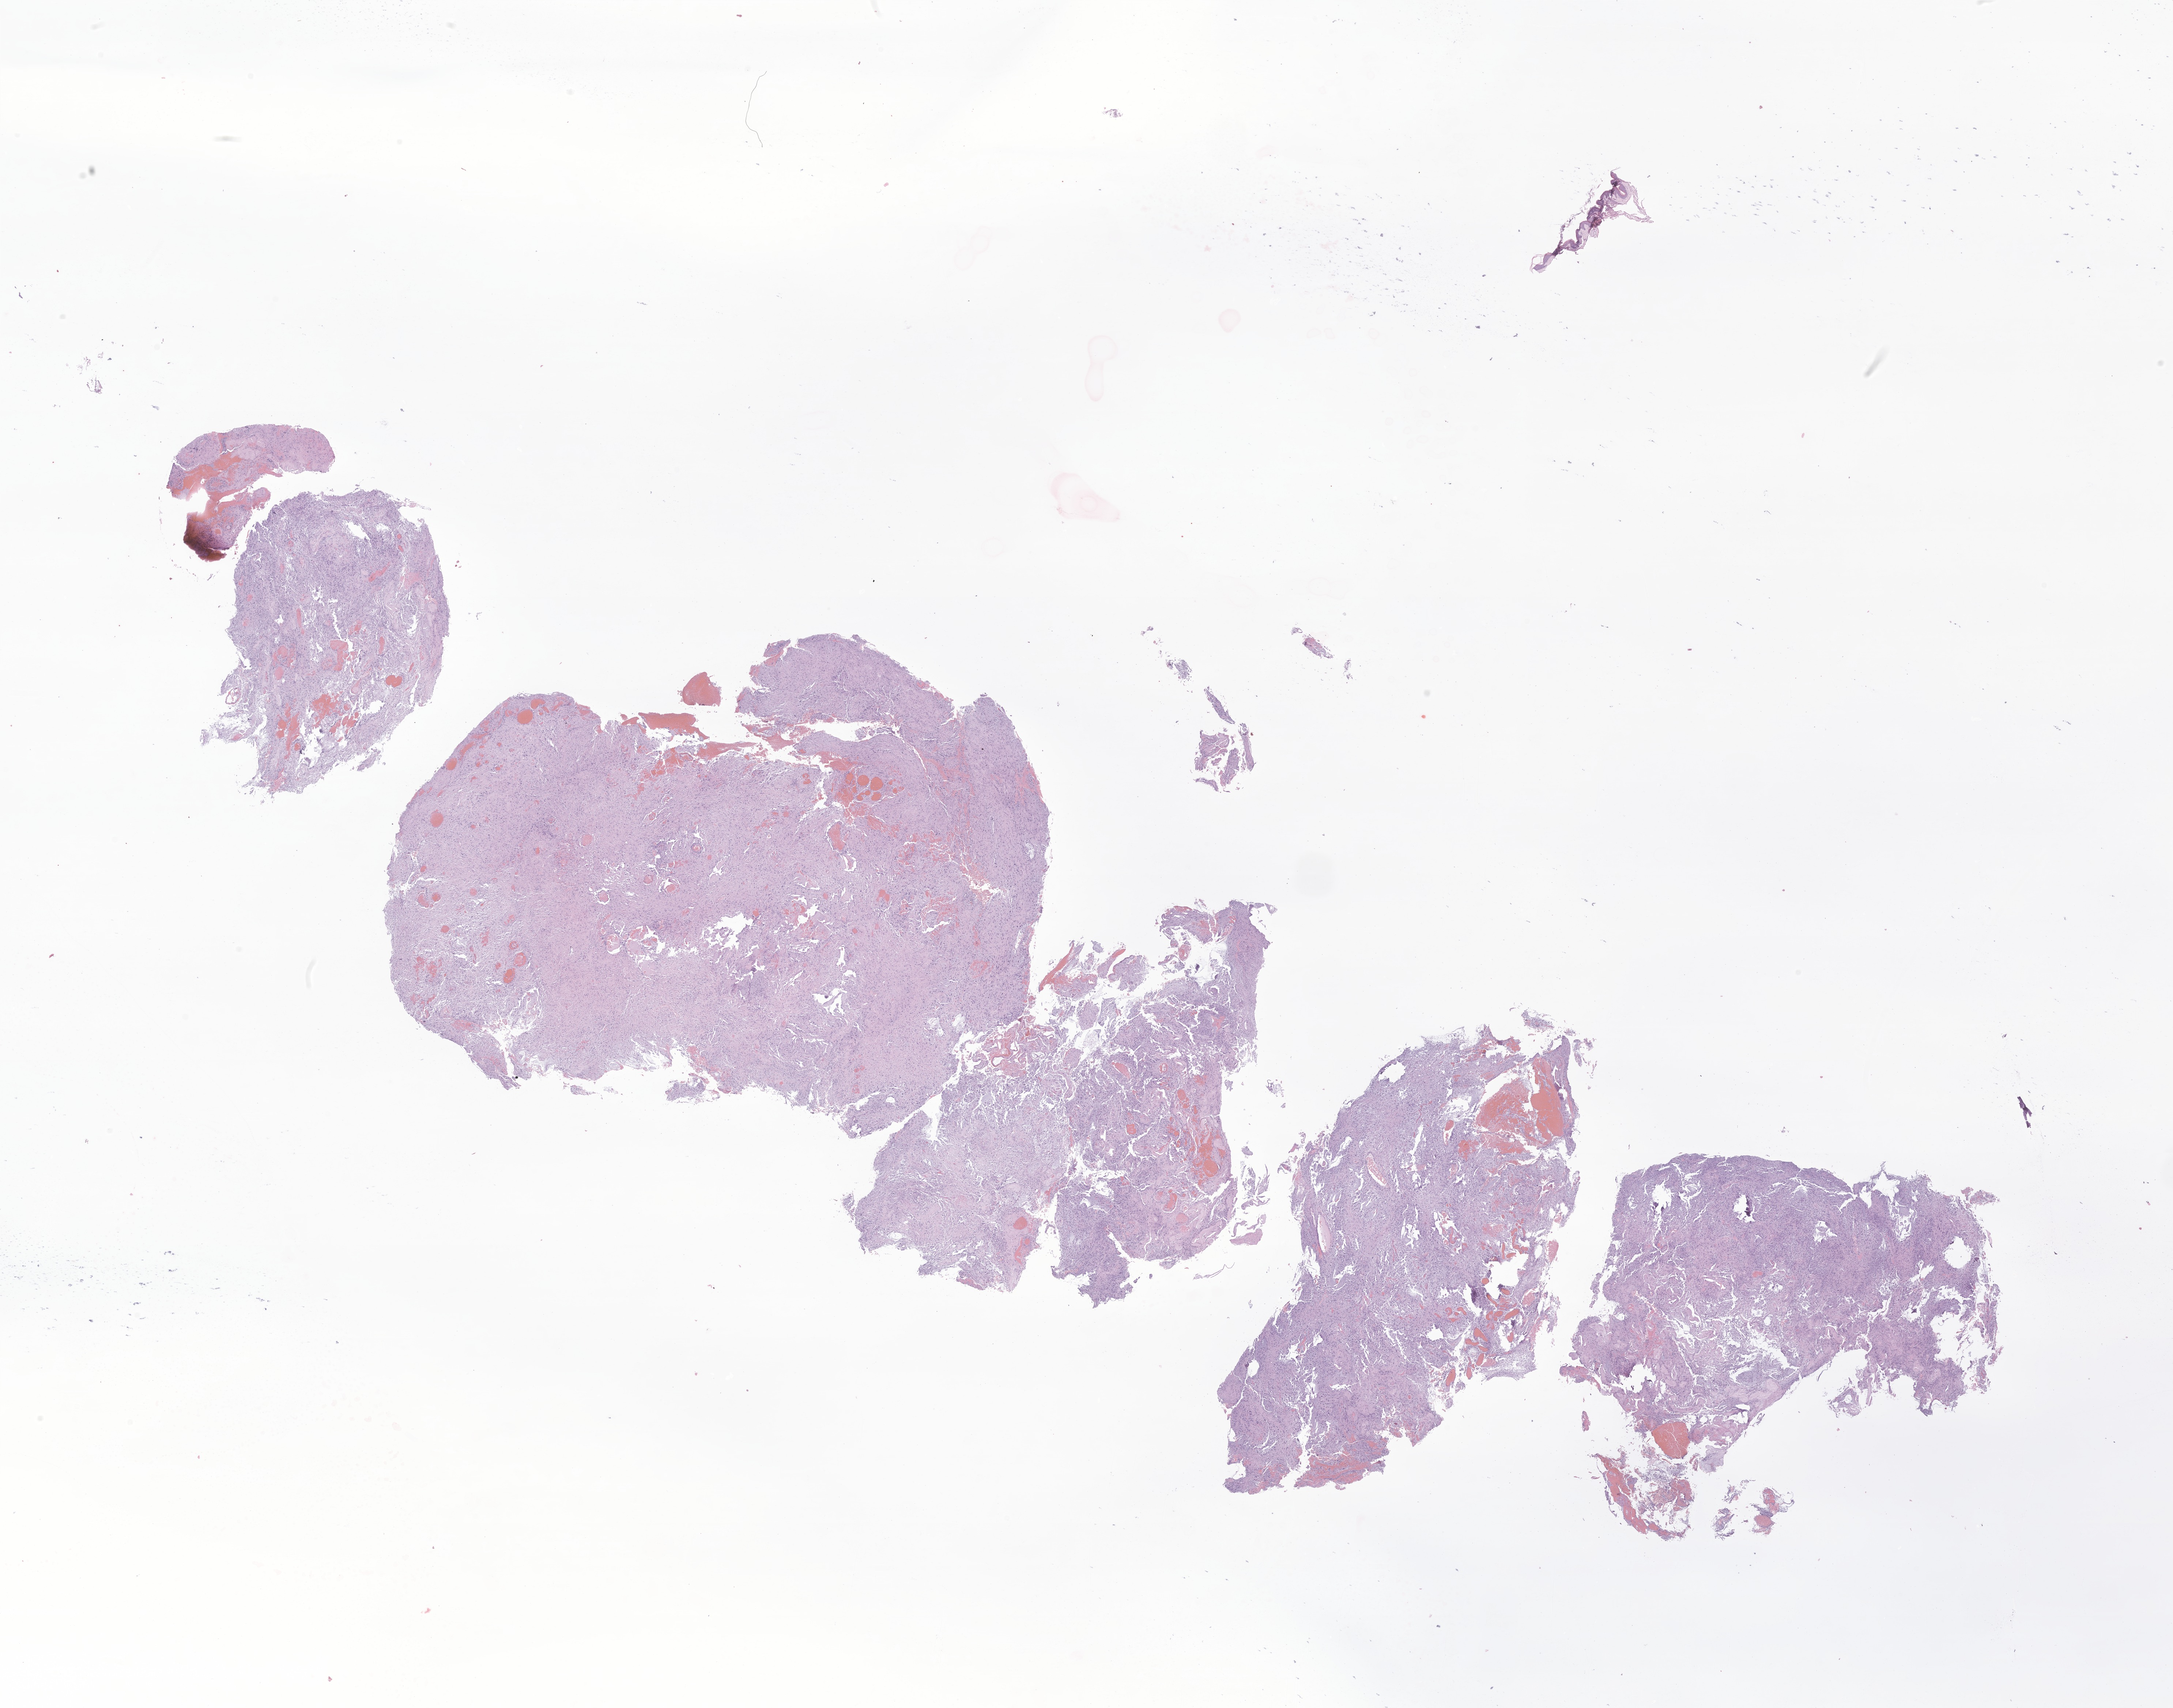
Hematoxylin and eosin (H&E) whole-slide image of tumor tissue from the temporal lobe — a low-resolution overview of the entire scanned area, about 25.1 x 19.7 mm; formalin-fixed paraffin-embedded section. Male patient, age 171 months (14 years 3 months).
Recorded diagnosis: Pilocytic astrocytoma.